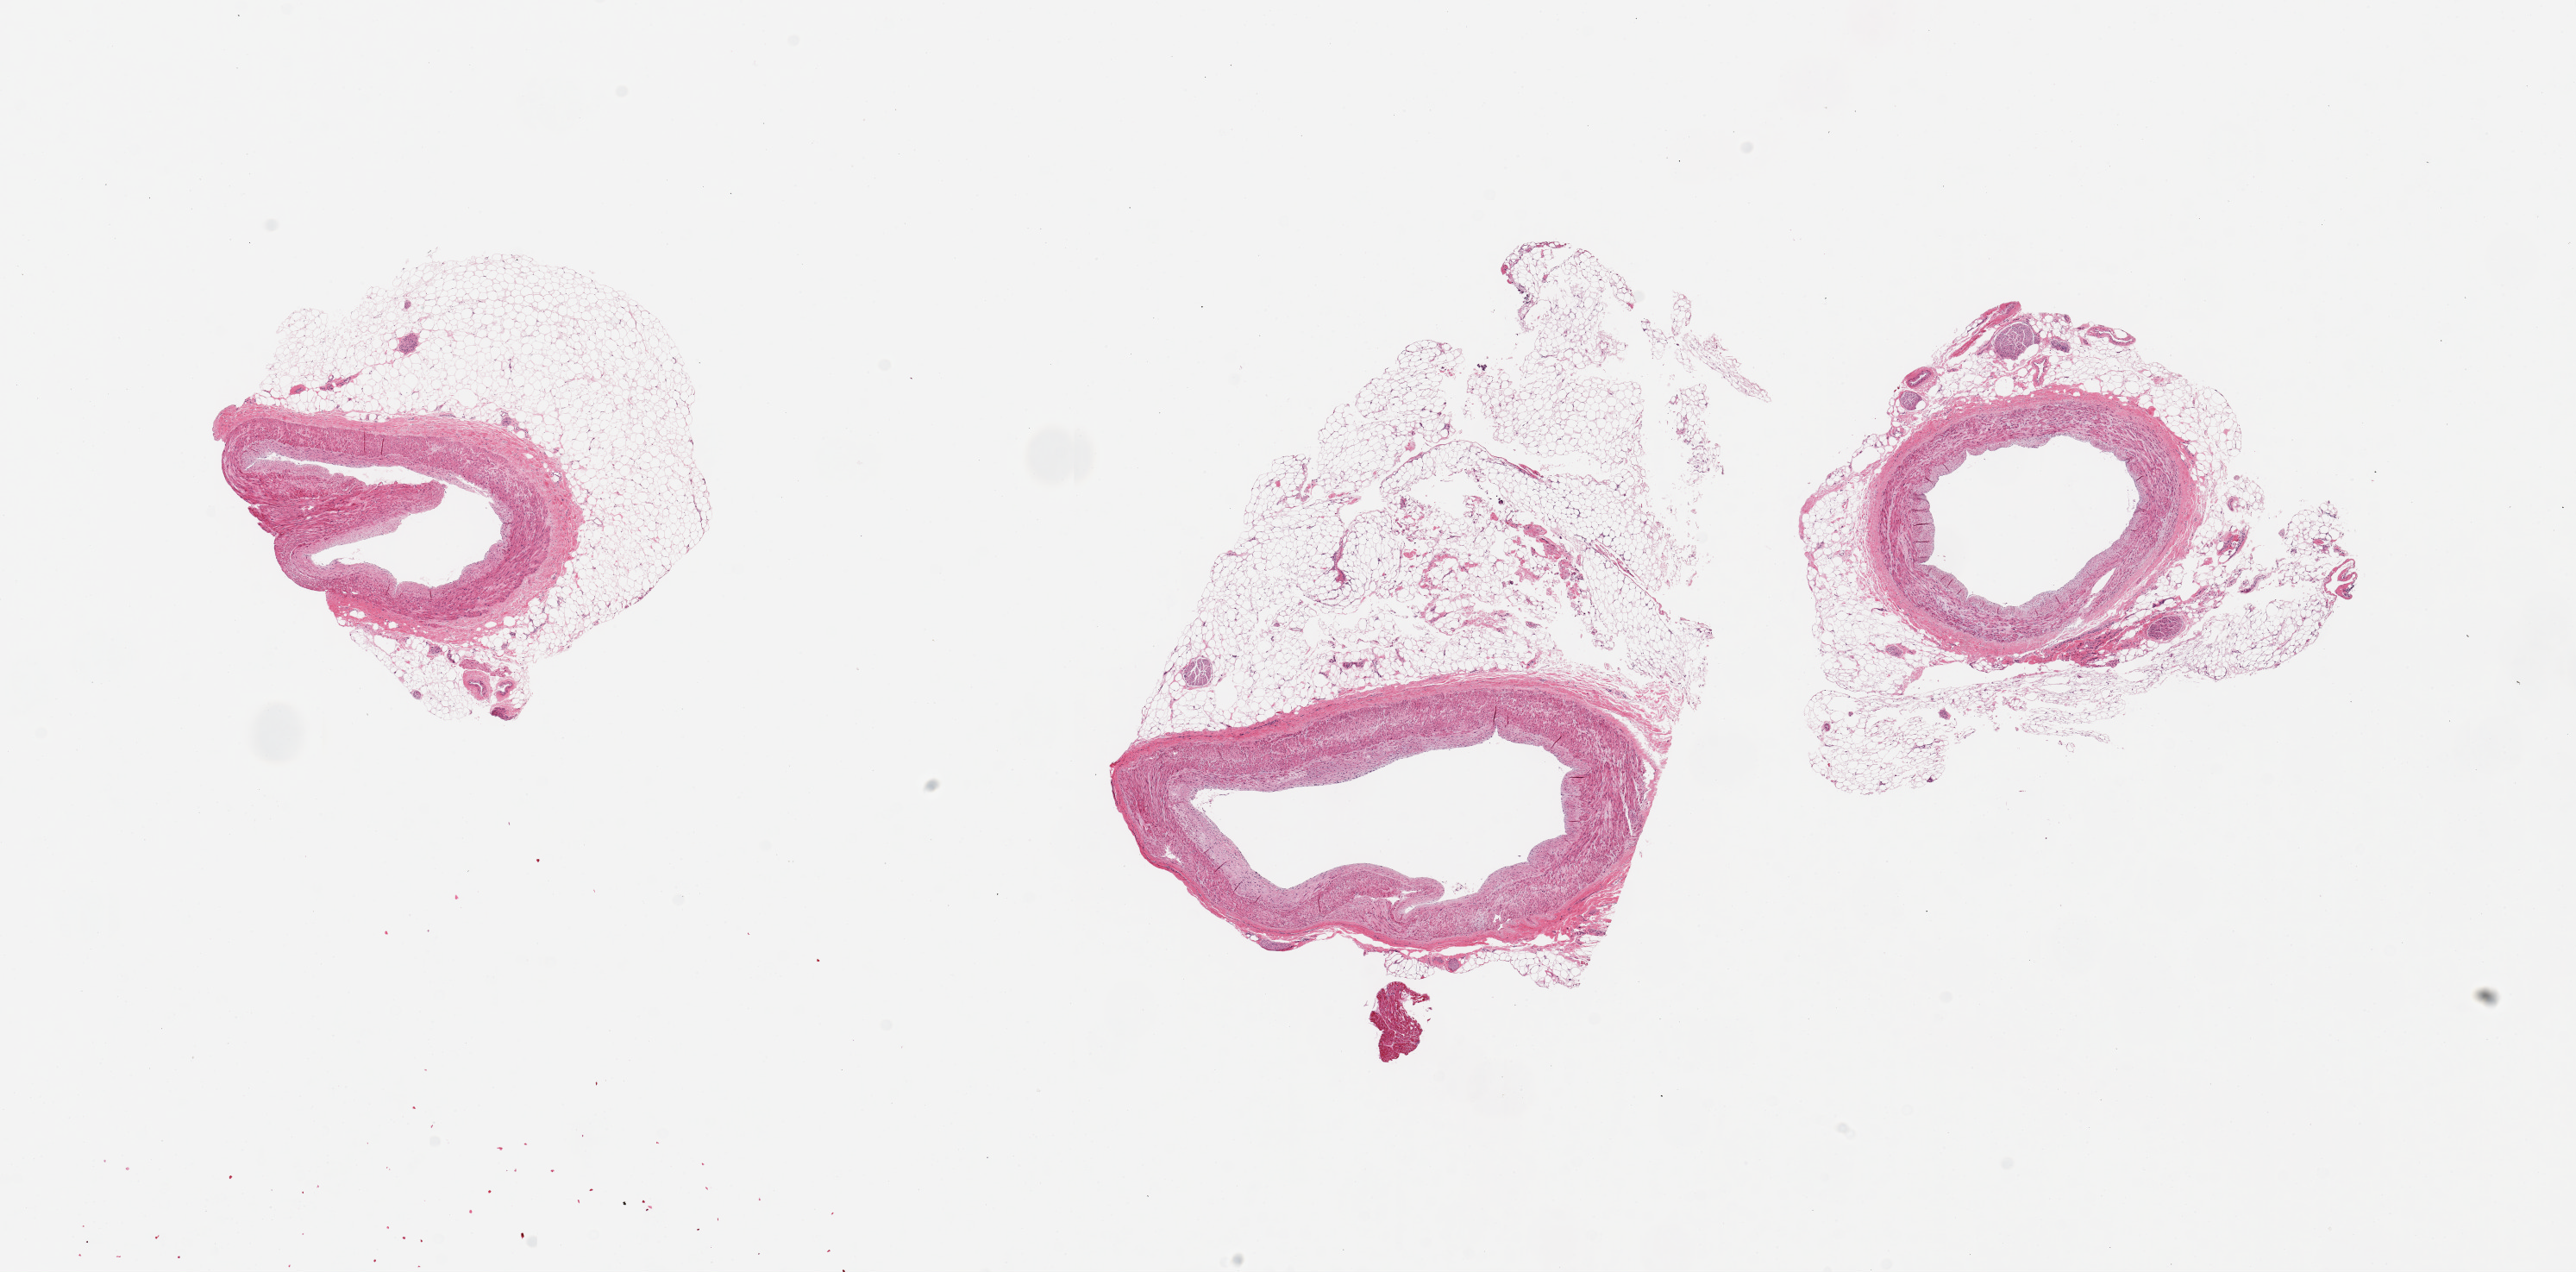
Hematoxylin and eosin (H&E) whole-slide image, brightfield — whole scanned area (about 23.6 x 11.7 mm) shown as a low-resolution overview. PAXgene-fixed paraffin-embedded (PFPE) section. Sampled site (target tissue): coronary artery. Tissue donor sample. Donor sex: male.
Review note (as recorded): 3 pieces, up to 8x5mm; Excessive extraneous adipose, up to 60% of tissue.